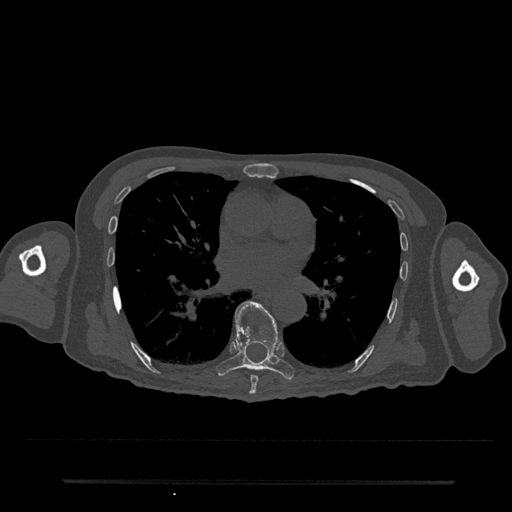
CT including the spine, one axial slice. Reconstruction kernel Br40s/3. 120 kVp. Bone window (W 1800 / L 400 HU). 0.5 mm slice thickness. 512 × 512 image matrix, field of view 427 × 427 mm. Patient: male, 74 years. Case-level facts recorded for this patient, not image findings: primary cancer: prostate.
Structures marked on this image (semi-automatic segmentation, software-assisted and operator-edited):
- T7 vertebra: box from (x=249, y=376) to (x=258, y=395) px
- T8 vertebra: (x=216, y=301)–(x=294, y=381)